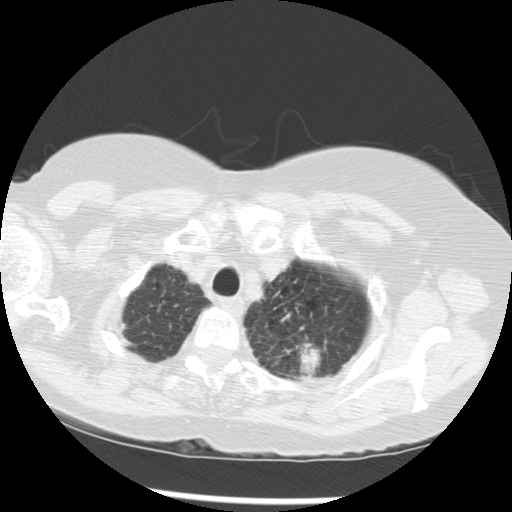
Low-dose screening chest CT, one axial slice. Position 247 of 283 along the scan axis. Lung window (W 1500 / L -600 HU). 2.5 mm slice thickness. 512 × 512 image matrix, field of view 330 × 330 mm.
Outlined on this slice (expert manual segmentation):
- lesion 1 (tumor, upper lobe of left lung): bounding box (x1, y1, x2, y2) in pixels: (298, 343, 322, 376)